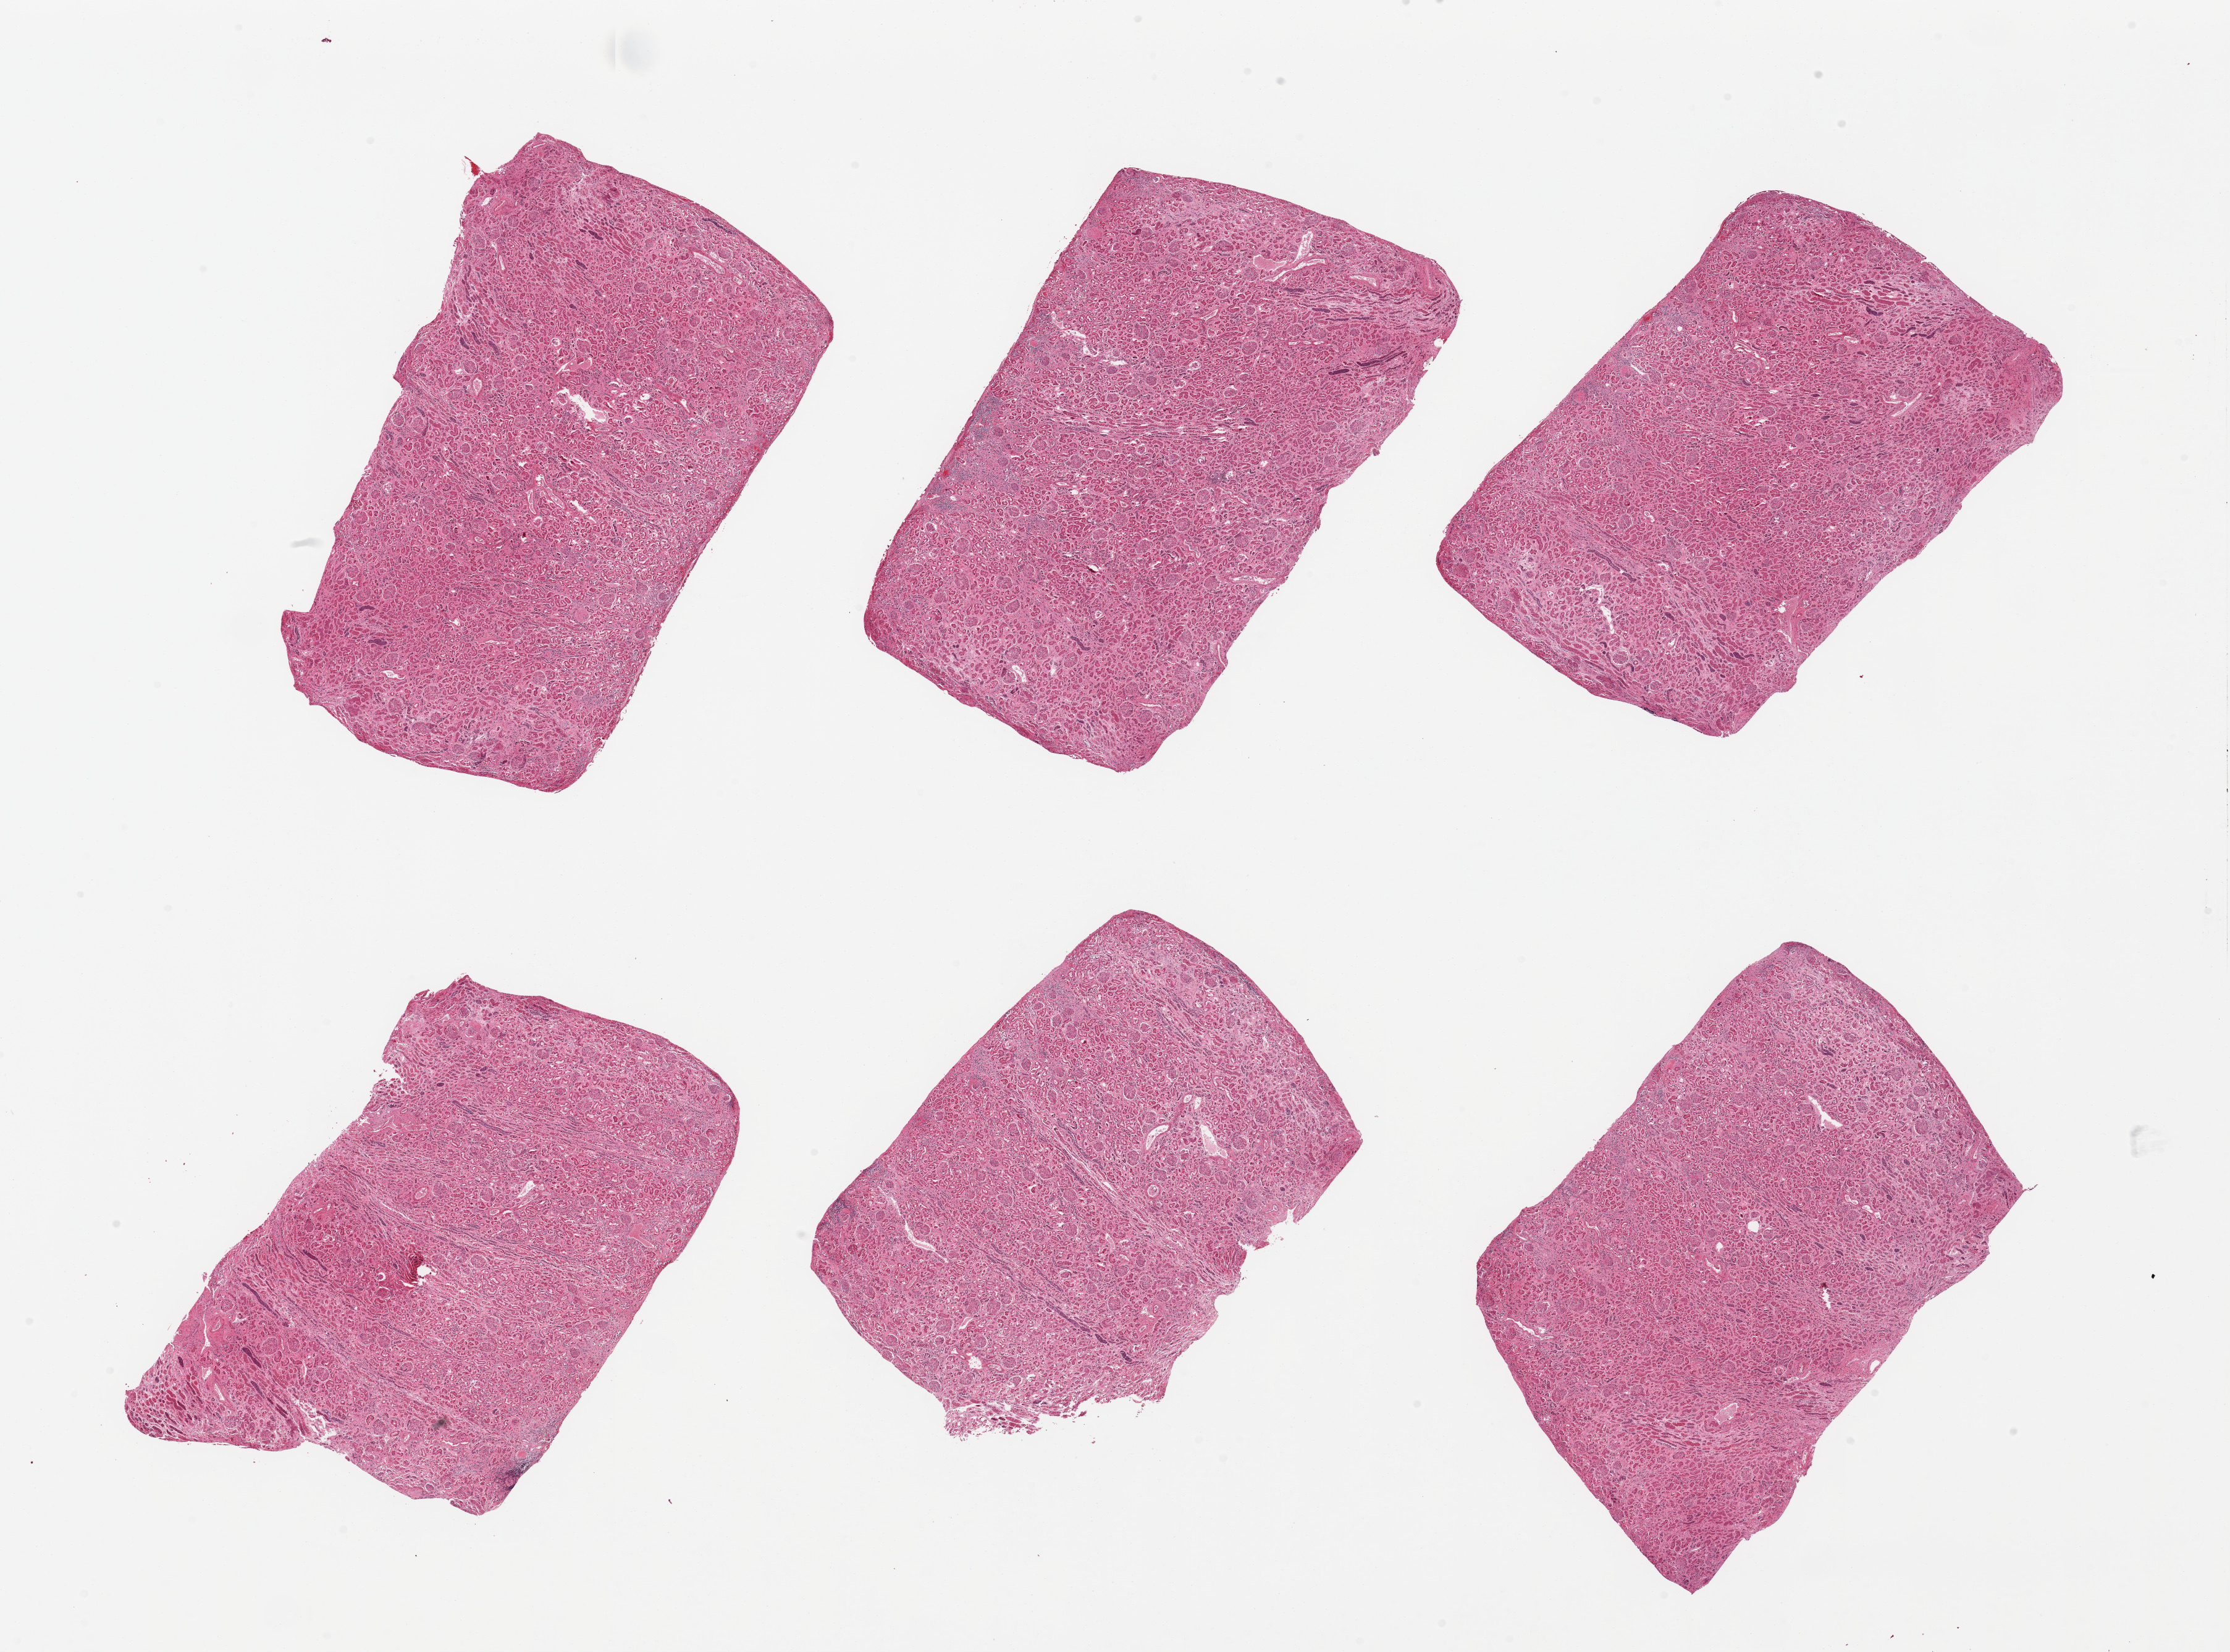
H&E whole-slide image, brightfield — low-resolution overview of the scanned area, about 28.5 x 21.2 mm; PAXgene-fixed paraffin-embedded (PFPE) section; section of renal cortex (target tissue); tissue donor sample. Donor sex: male.
Pathologist's review note for this sample: 6 pieces; tubules and ducts severely autolyzed; glomeruli somewhat better preserved; no sign of chronic or acute lesions.